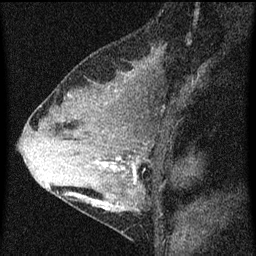
Breast MRI (dynamic contrast-enhanced), one sagittal slice. Slice 30 of 60 in the series (ordered by position). Dynamic contrast-enhanced series, image 2 of 3 at this slice position (ordered by acquisition). 1.5 T. TE 4.2 ms, TR 8 ms. 256 × 256 image matrix, field of view 180 × 180 mm. Female patient, age 33 years.
Annotated regions visible in this slice (semi-automatic segmentation, software-assisted and operator-edited):
- analysis volume of interest (the breast-tissue region the enhancement analysis was run in; not a lesion): bounding box [x1, y1, x2, y2] px = [67, 118, 156, 213]
- tumour enhancement mask (voxels above the 70 % enhancement threshold inside the analysis volume of interest): [97, 158, 136, 211]